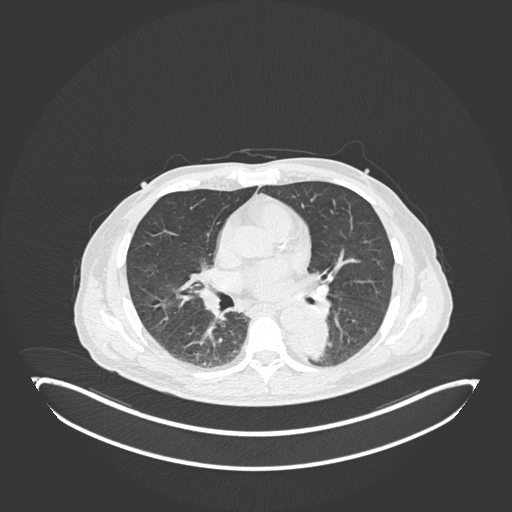
Chest CT, one axial slice. Reconstruction kernel B30f. Lung window (W 1500 / L -600 HU). 1 mm slice thickness. 512 × 512 image matrix, field of view 500 × 500 mm. Male patient, age 72 years. Case-level facts recorded for this patient, not image findings: clinical TNM (as recorded): T2b N0 M1.
Annotated regions visible in this slice (rectangle marked by the reading radiologist):
- lung tumour (recorded histology: adenocarcinoma): bounding box <283,312,329,363> (left, top, right, bottom; pixels)